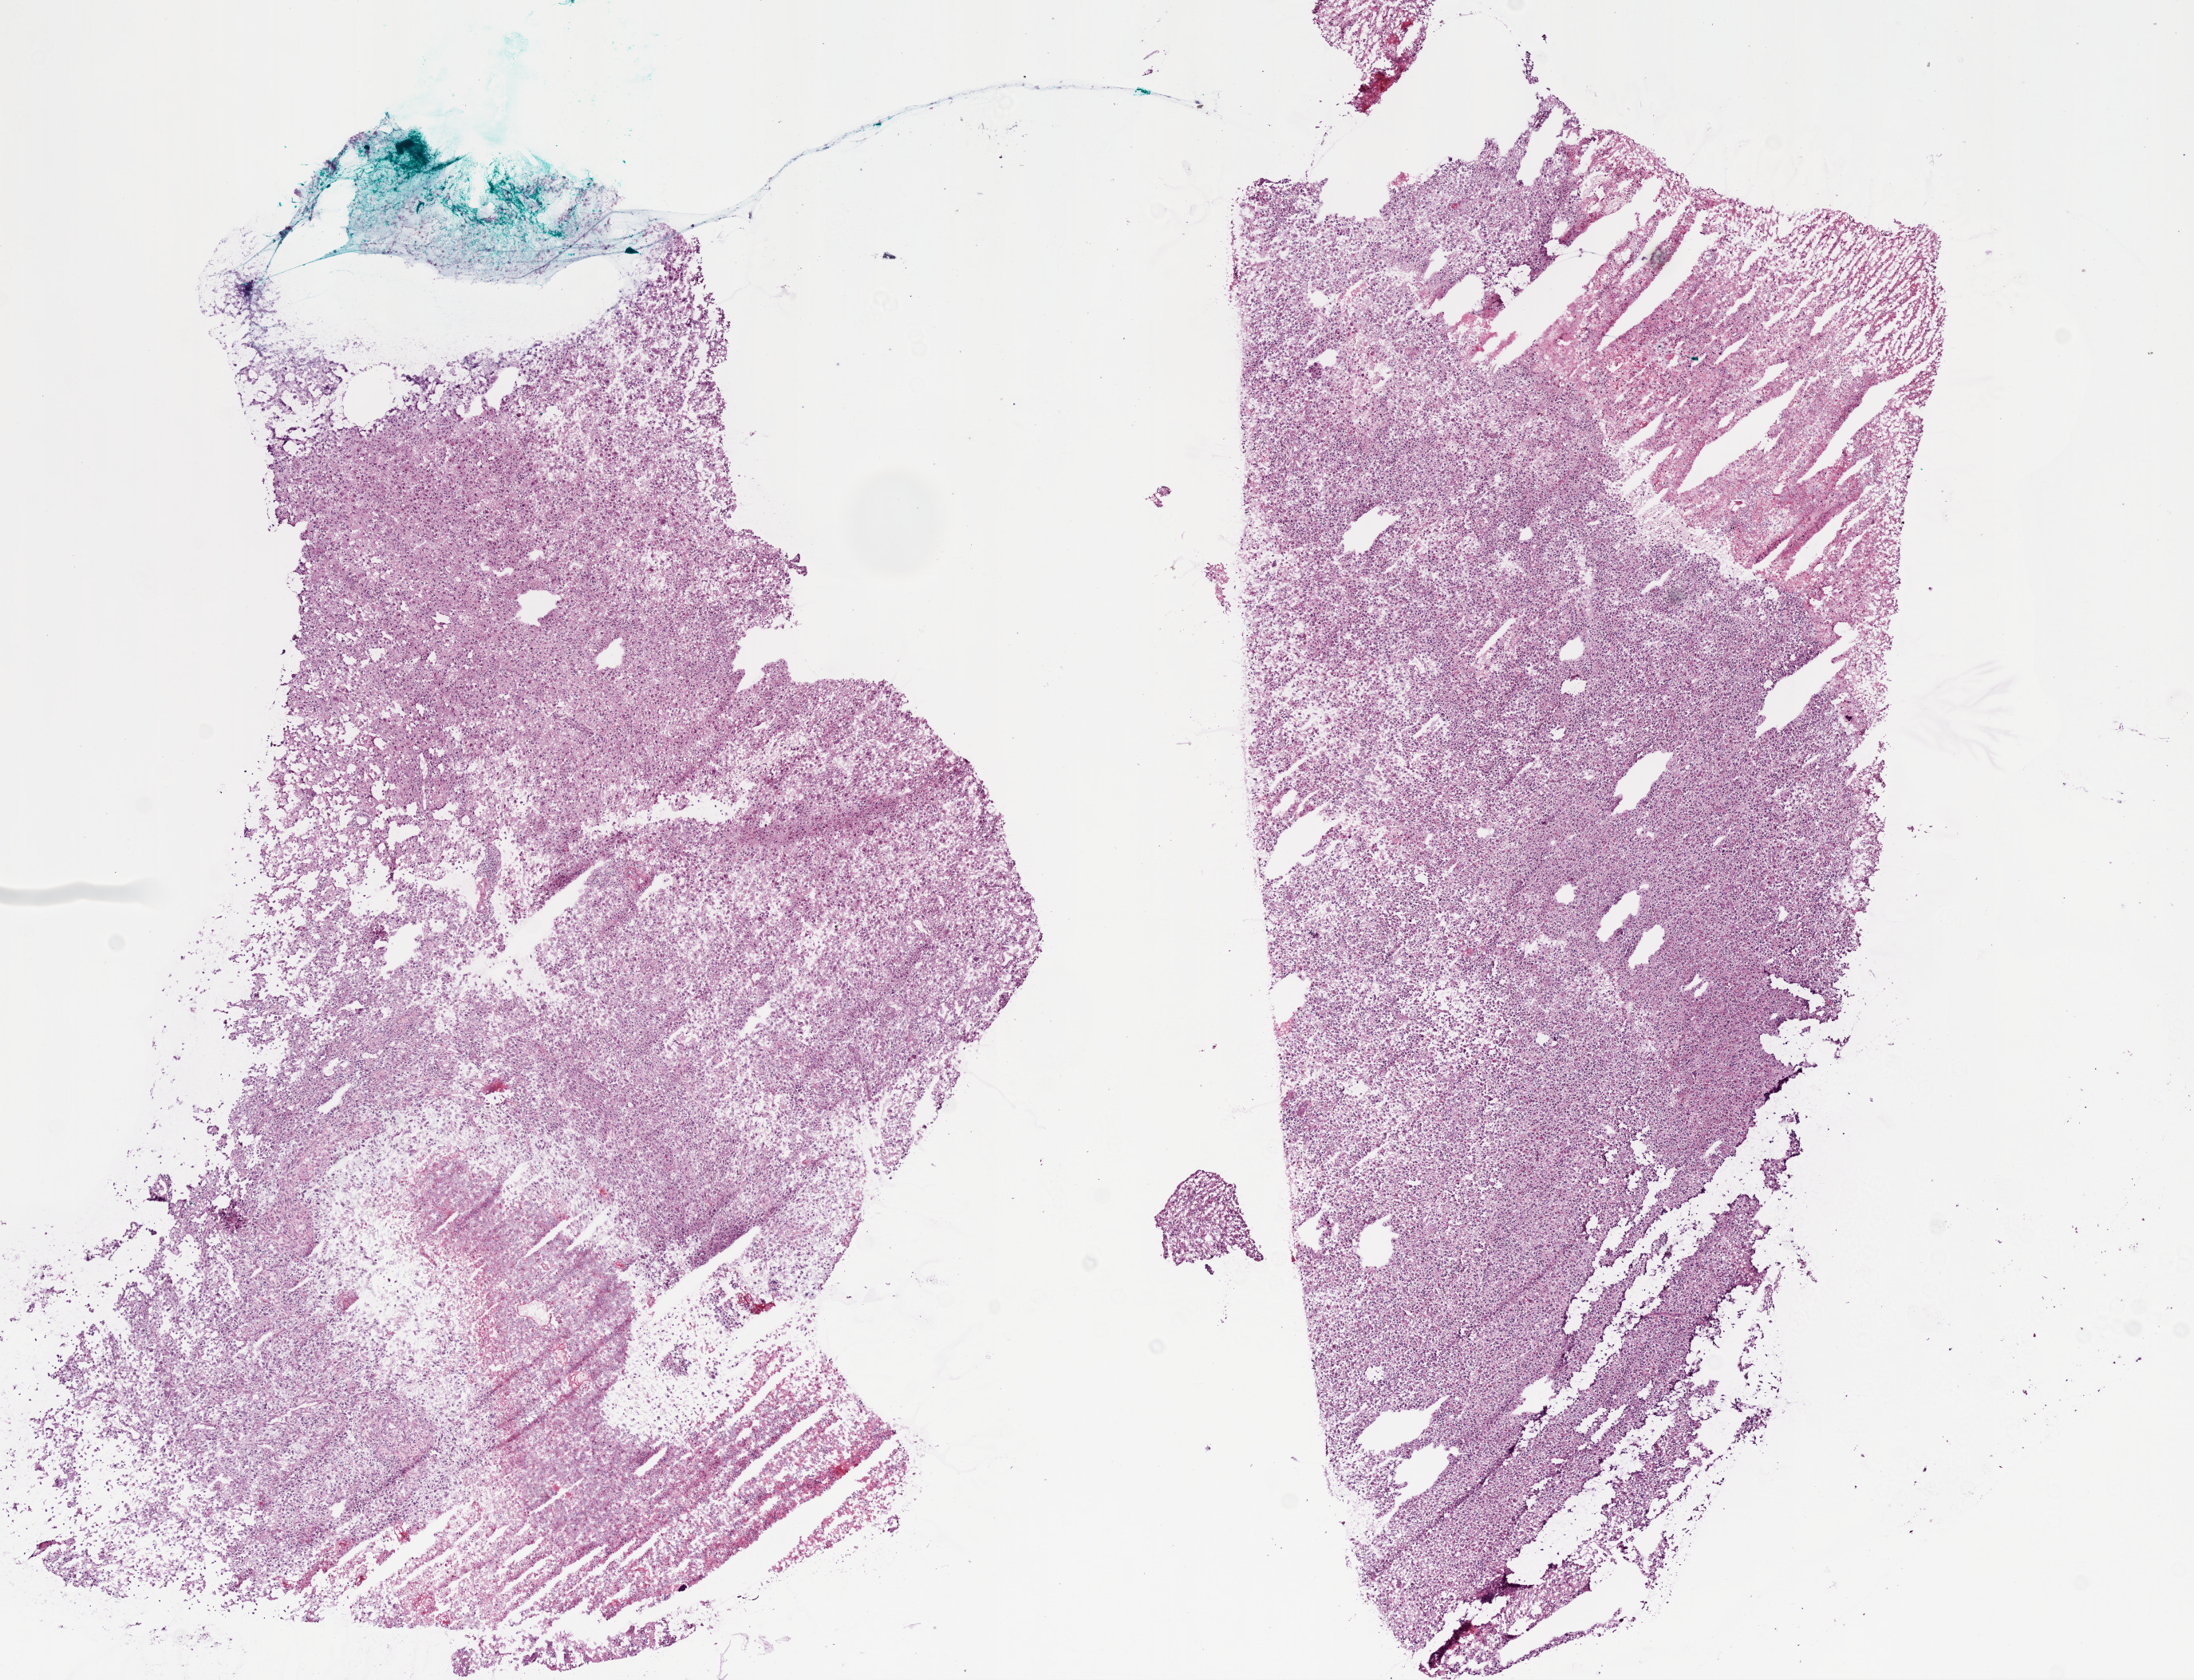
H&E-stained whole-slide image, a low-resolution overview of the entire scanned area, about 11.0 x 8.4 mm; frozen section from the bottom of the tissue portion; sample: primary tumour, brain. Patient: female, age at initial diagnosis 49 years. Composition of this section per pathologist review: tumour cells 75%, tumour nuclei 95%, normal cells 0%, stromal cells 0%, necrosis 25%.
Histologic diagnosis: Glioblastoma.